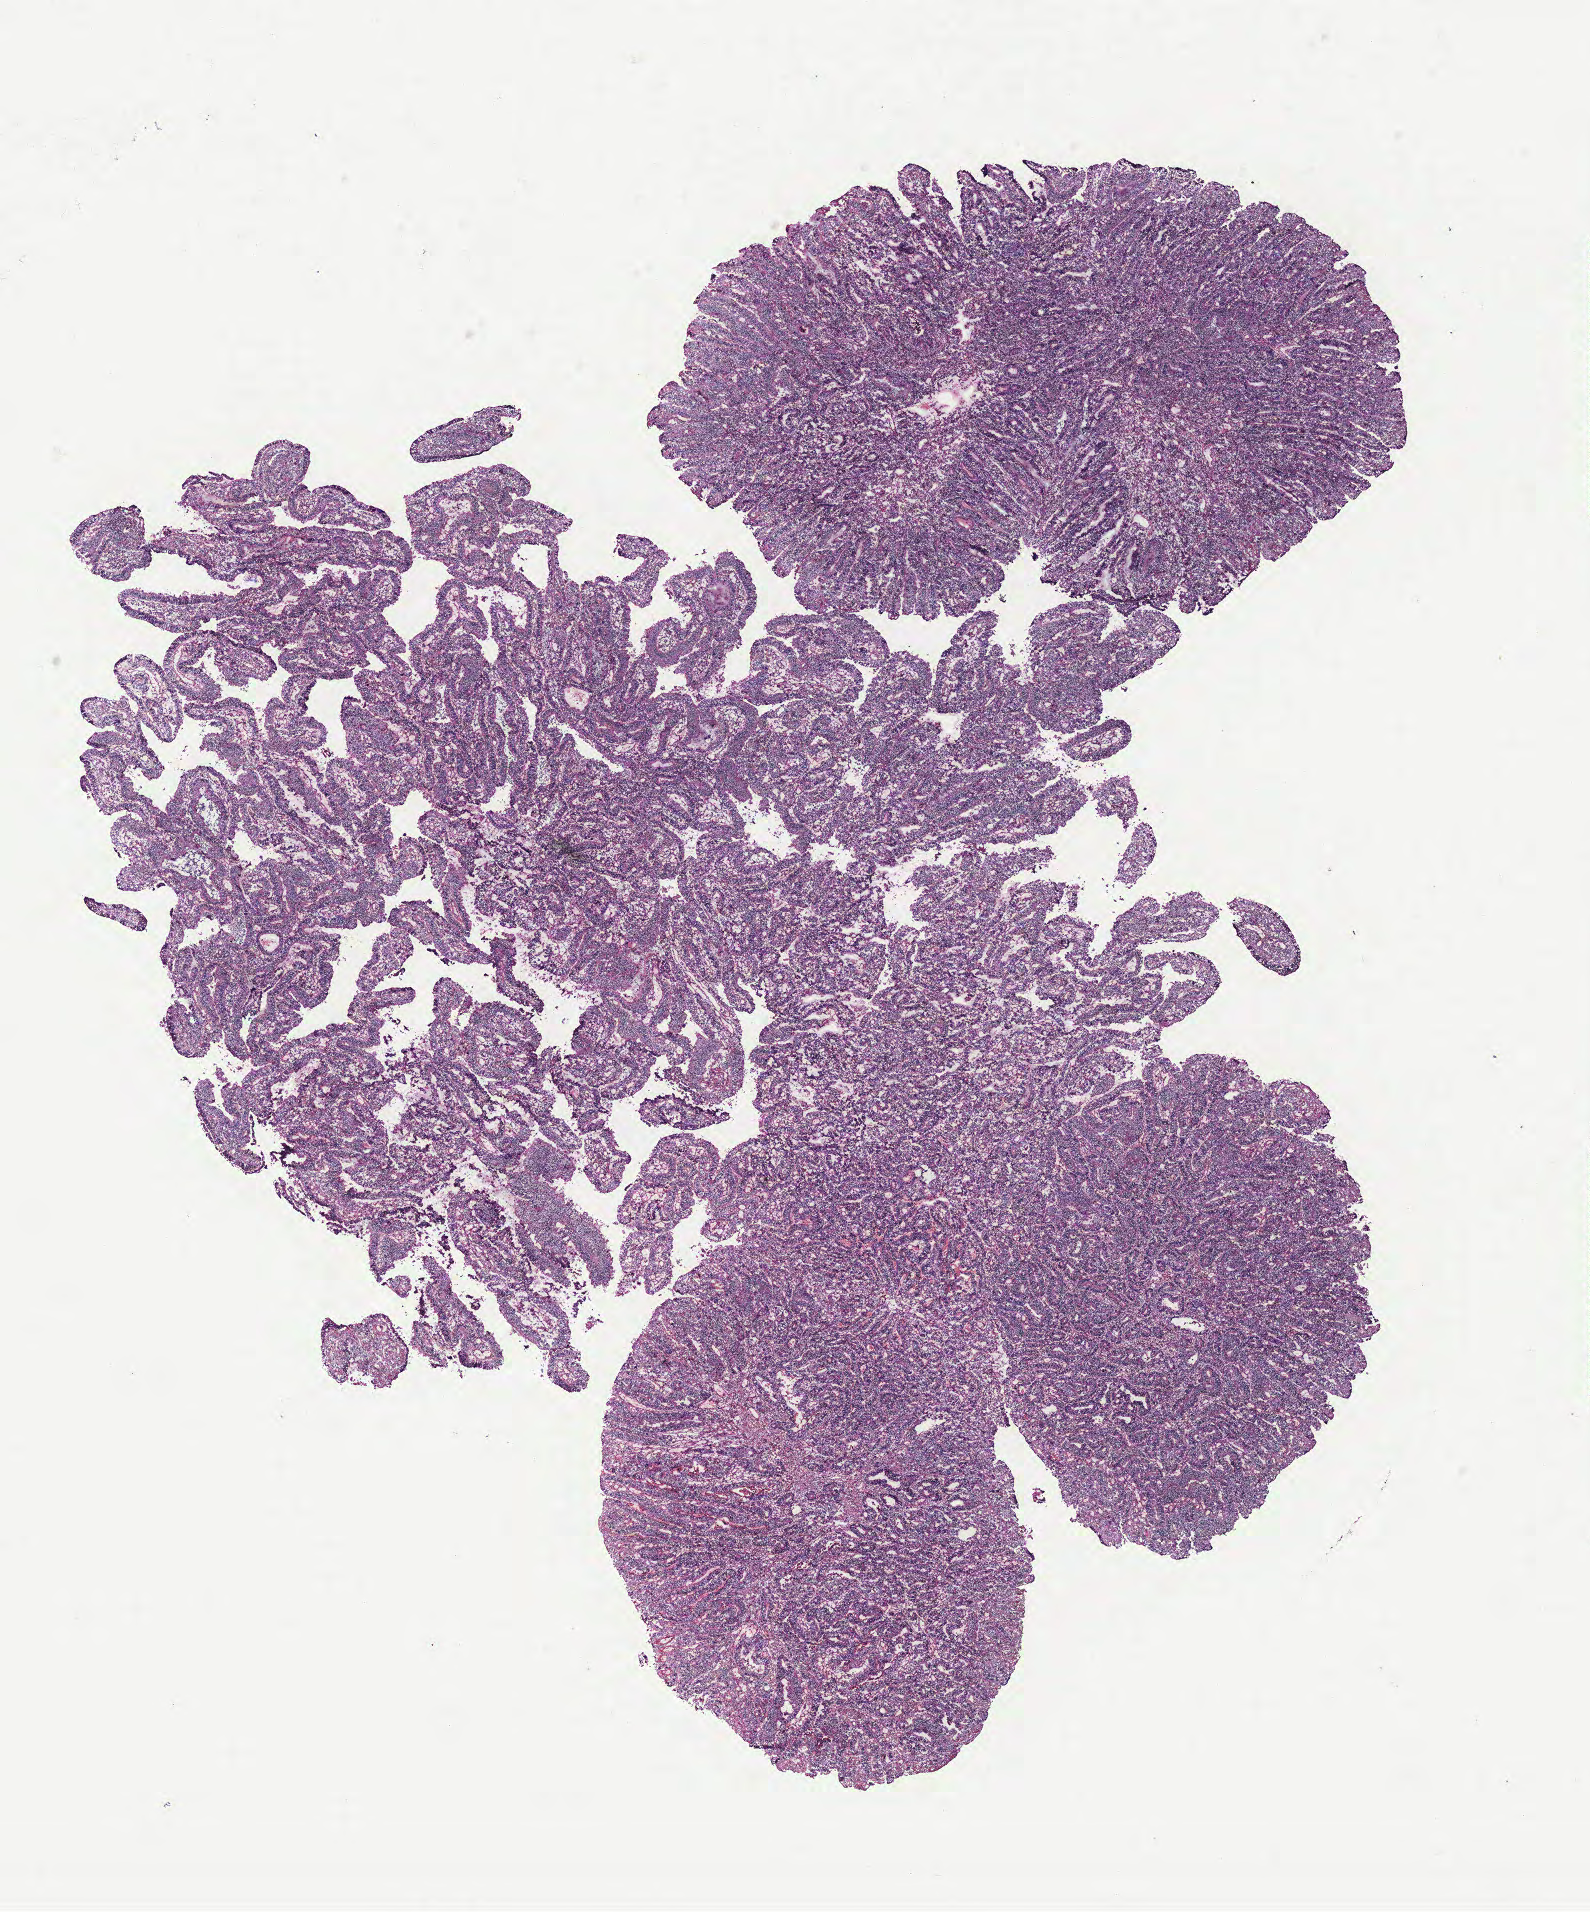
Digitized Hematoxylin and eosin (H&E) stained tissue section (whole slide) — a low-resolution overview of the entire scanned area, about 12.7 x 15.3 mm (from a 40x scan); colon, tissue type not recorded.
Patient diagnosis (cohort enrolment): colon cancer (colon).